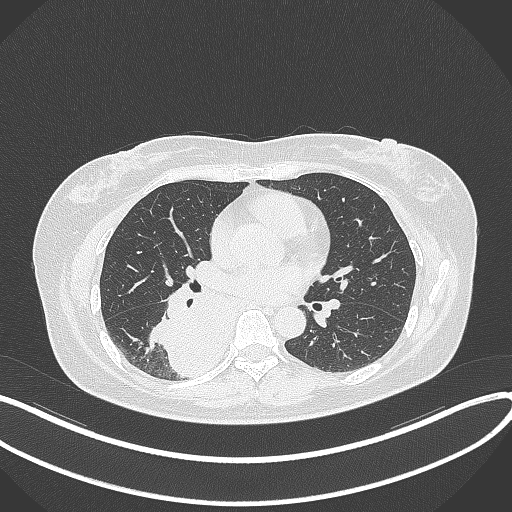
Chest CT, one axial slice. Position 181 of 331 along the scan axis. Reconstruction kernel B70f. 120 kVp. Lung window (W 1500 / L -600 HU). 1 mm slice thickness. 512 × 512 image matrix, field of view 400 × 400 mm. Patient: female, 54 years. Case-level facts recorded for this patient, not image findings: clinical TNM (as recorded): T4 N0 M0.
Outlined on this slice (rectangle marked by the reading radiologist):
- lung tumour (recorded histology: adenocarcinoma): box from (x=150, y=285) to (x=228, y=378) px